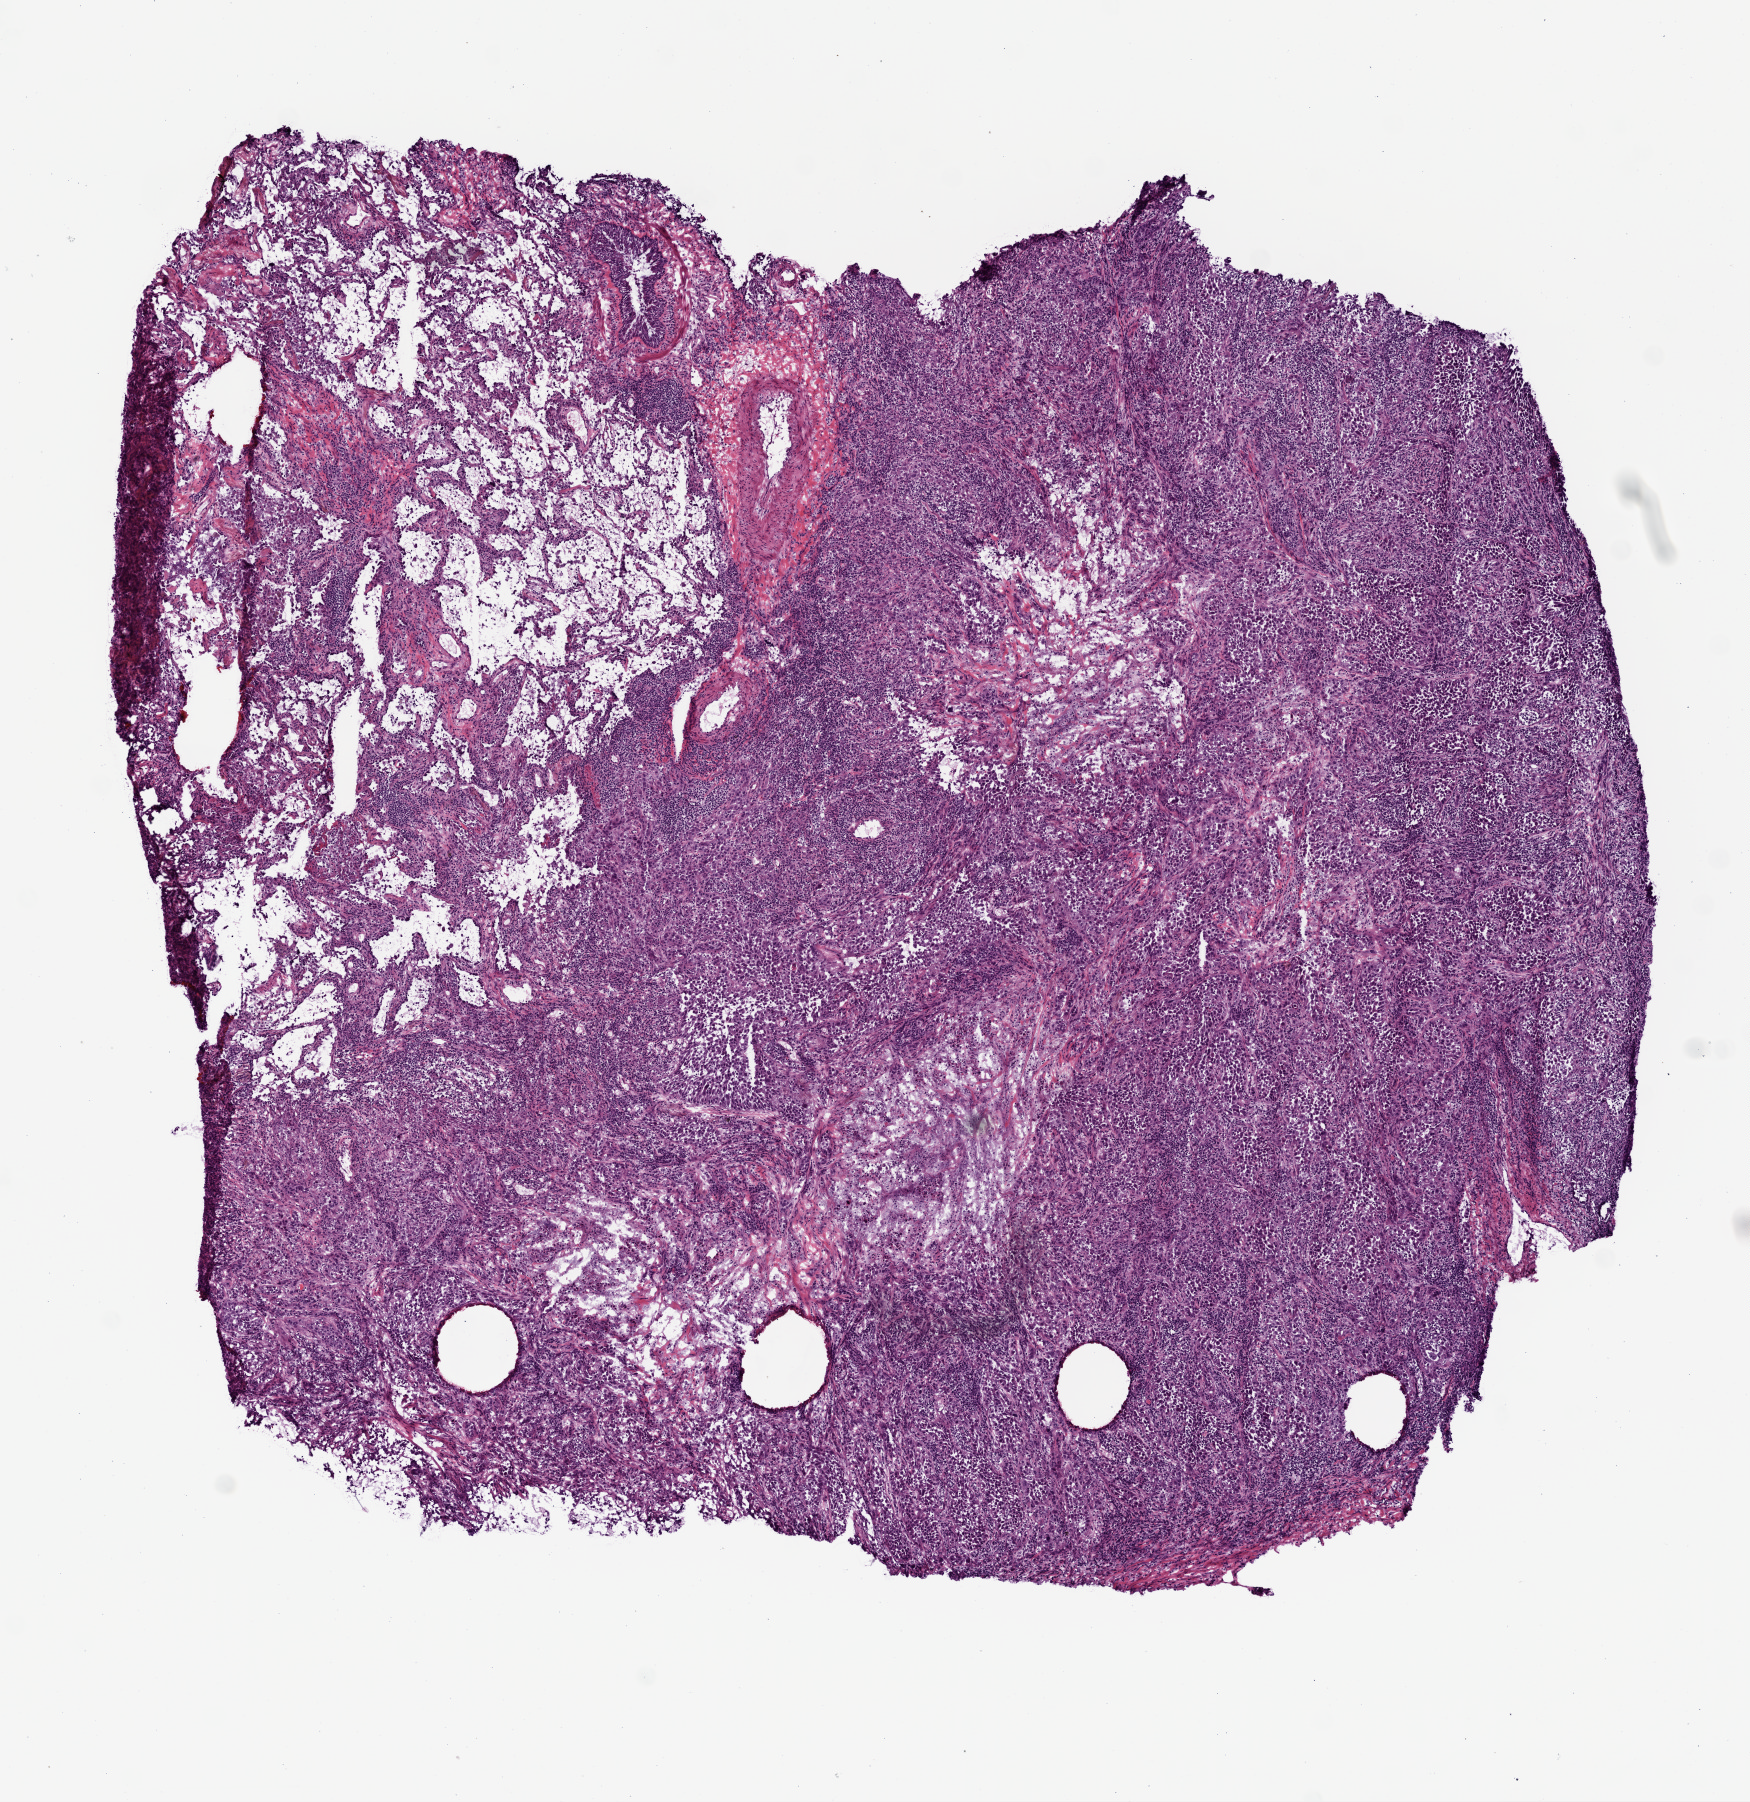
Hematoxylin and eosin (H&E) stained whole-slide image — shown as a low-resolution overview of the whole scanned area (about 7.0 x 7.2 mm), frozen section from the top of the tissue portion, sample: primary tumour, lung. Male patient; age at initial diagnosis 56 years. Slide review estimates, as recorded: tumour cells 90%, tumour nuclei 60%, normal cells 0%, stromal cells 5%, necrosis 5%.
Laterality: right. AJCC pathologic stage: IA (7th edition). Diagnosis: Adenocarcinoma, NOS (upper lobe, lung).